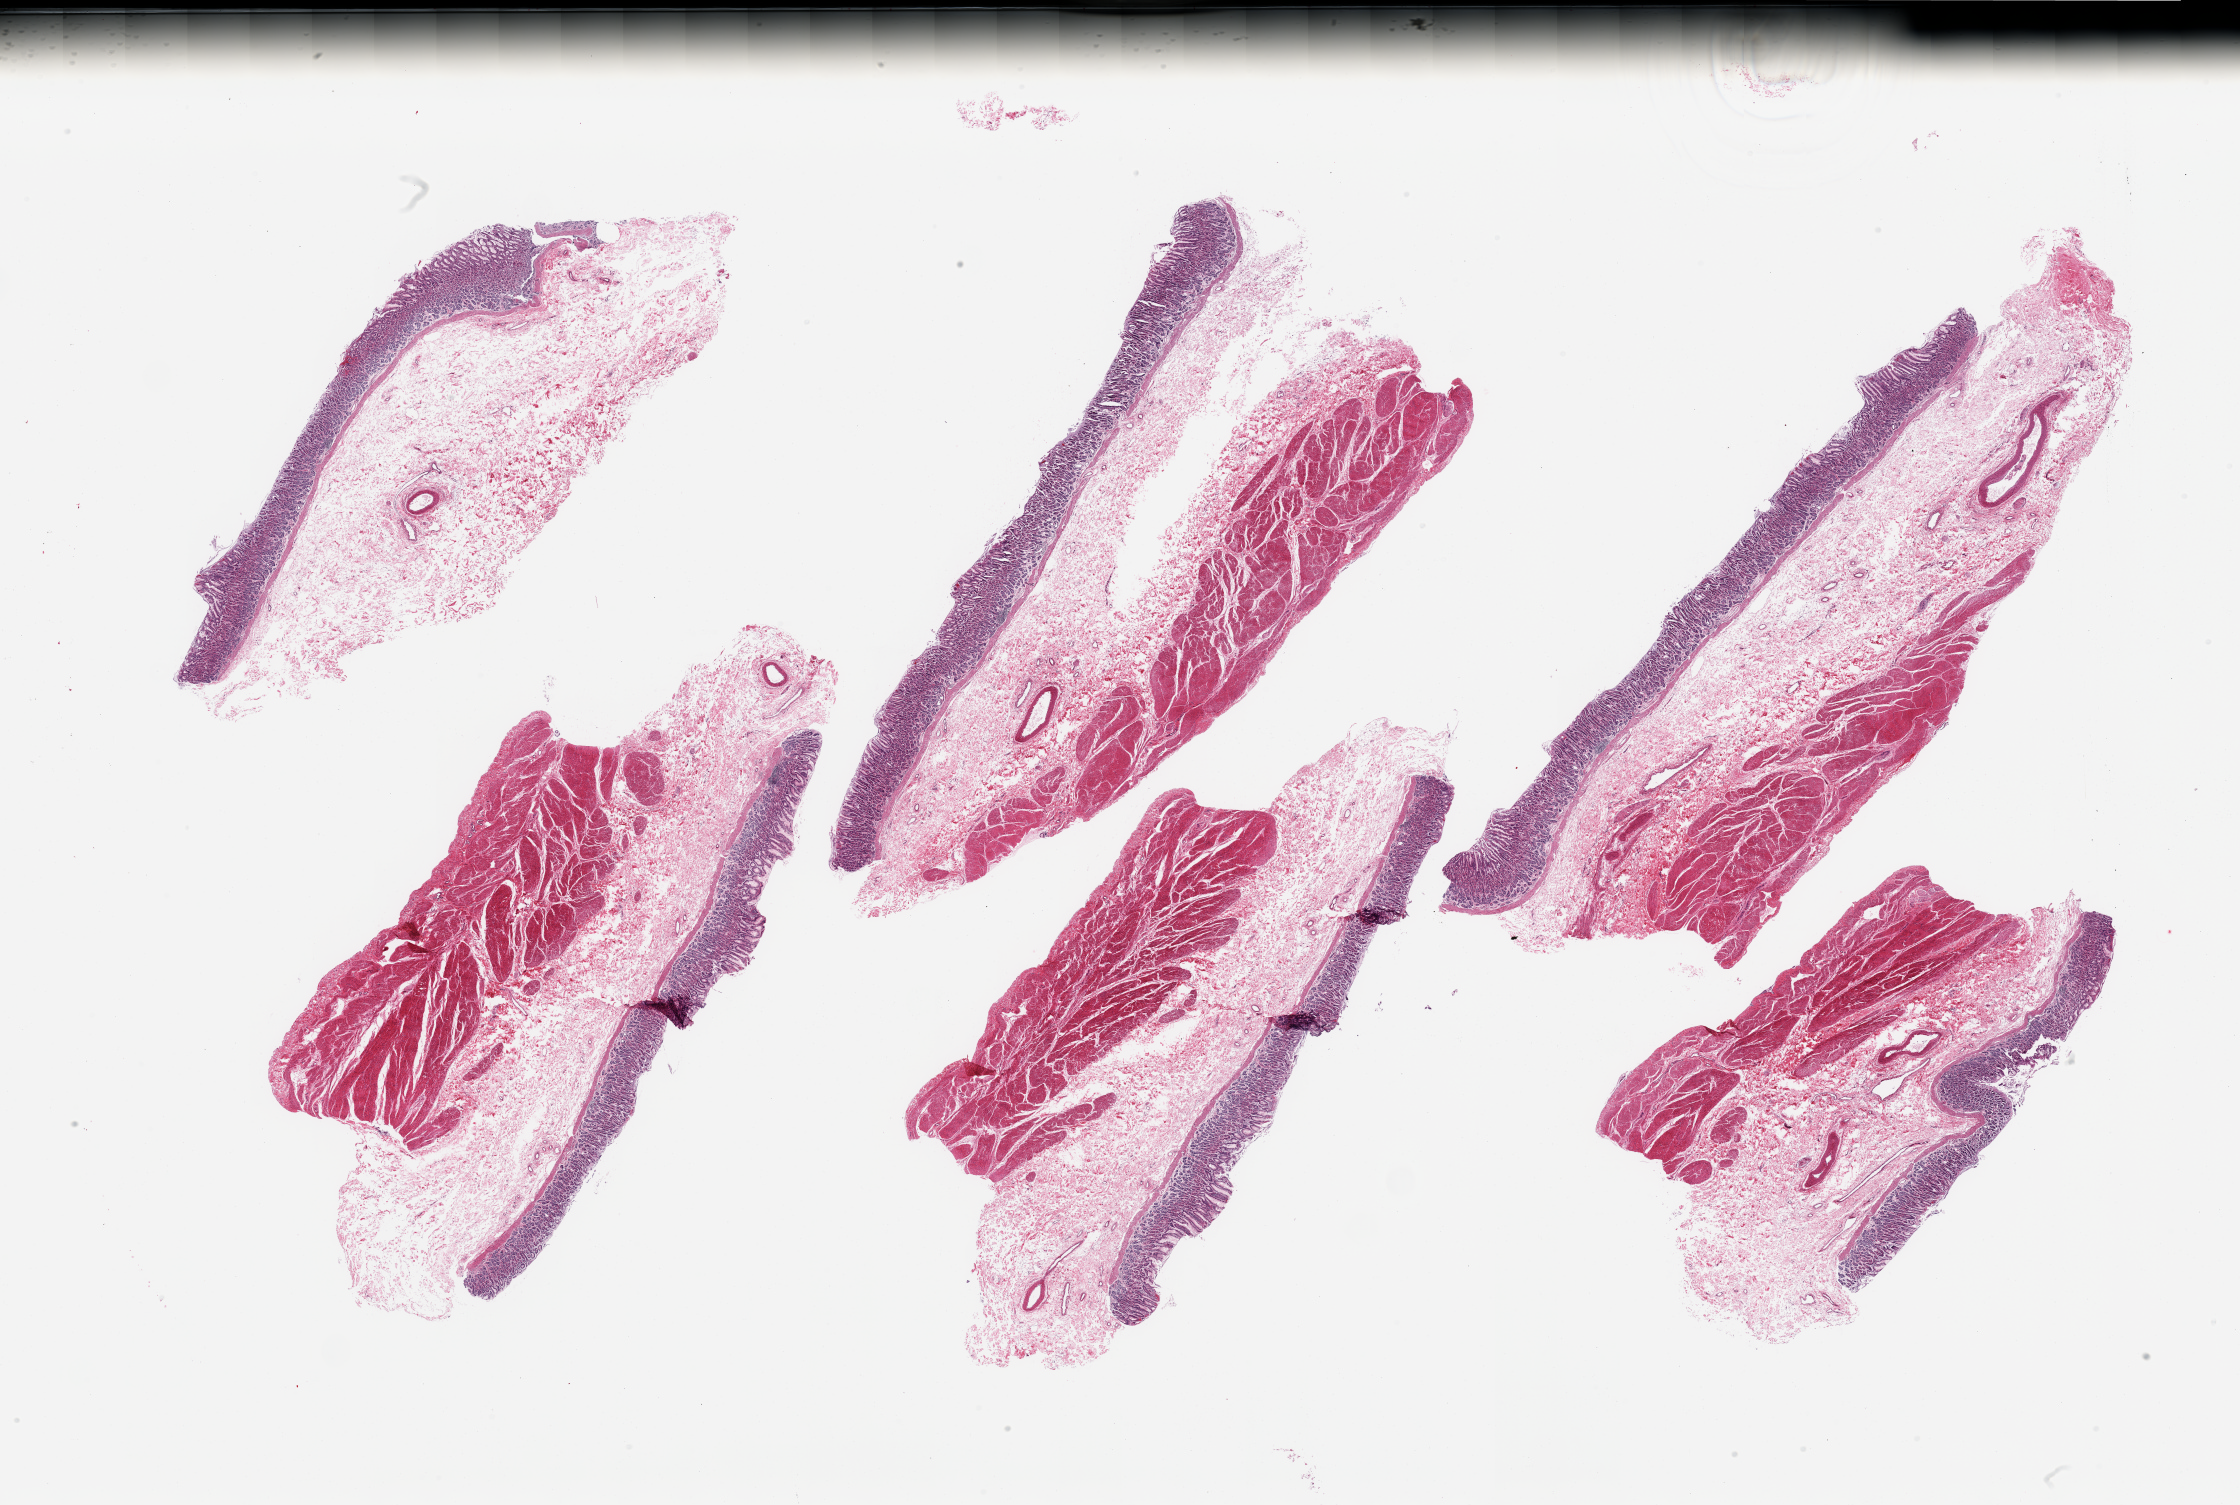
Hematoxylin and eosin (H&E) whole-slide image, whole scanned area (about 35.4 x 23.8 mm, acquisition: 20x scan) shown as a low-resolution overview. PAXgene-fixed paraffin-embedded (PFPE) section. Sampled site (target tissue): stomach. Tissue donor sample. Donor: female.
Pathologist's review note for this sample: 6 pieces; 5 of 6 have full thickness wall, 1 has no muscularis; submucosa edematous.